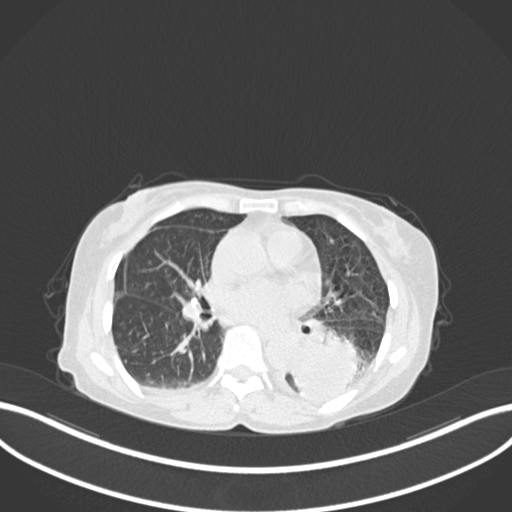
Chest CT, one axial slice; position 75 of 233 along the scan axis; reconstruction kernel B30f; 120 kVp; lung window (W 1500 / L -600 HU); 1 mm slice thickness; 512 × 512 image matrix, field of view 400 × 400 mm. Patient: female, 78 years. Case-level facts recorded for this patient, not image findings: clinical TNM (as recorded): T3 N0 M1.
Outlined on this slice (rectangle marked by the reading radiologist):
- lung tumour (recorded histology: squamous cell carcinoma): bounding box <287,333,363,400> (left, top, right, bottom; pixels)